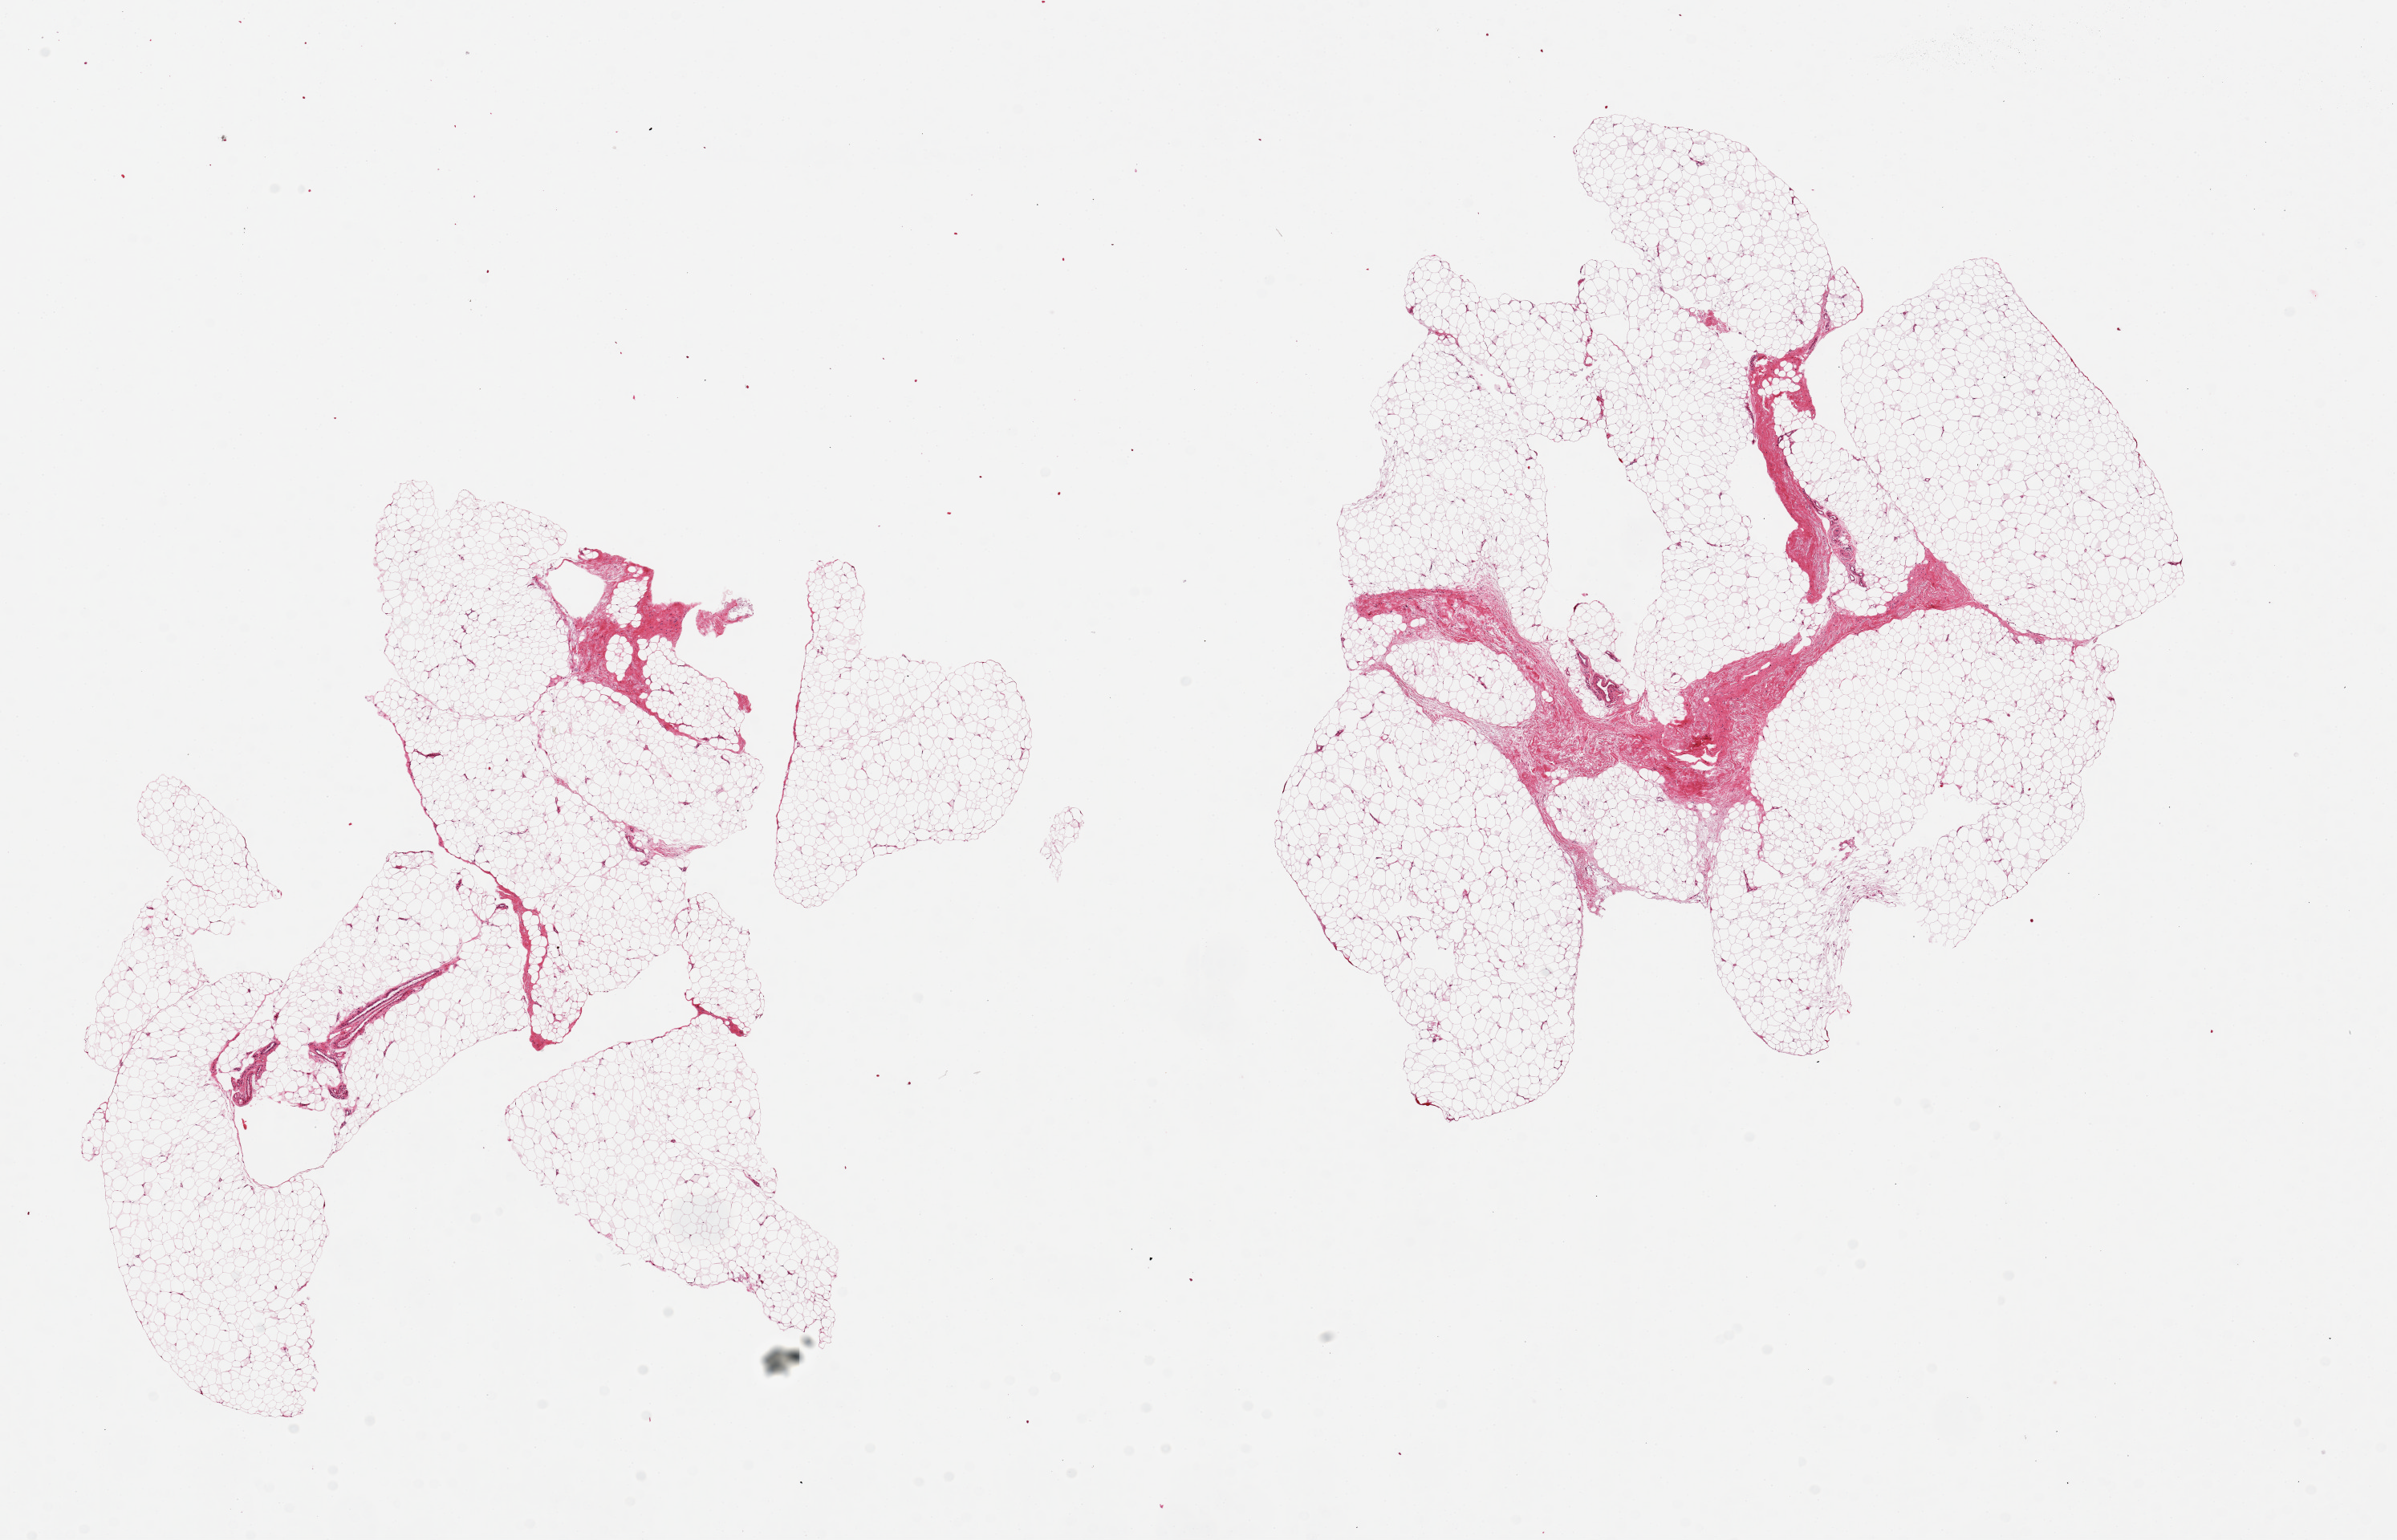
H&E whole-slide image — a low-resolution overview of the entire scanned area, about 23.6 x 15.2 mm (slide scanned at 20x); PAXgene-fixed, paraffin-embedded tissue; sampled site (target tissue): adipose tissue; donor tissue sample. Donor sex: male.
Pathologist's review note for this sample: 2 pieces ~10x8mm.